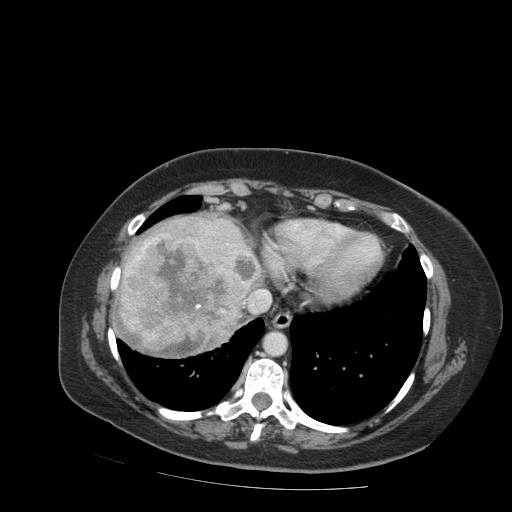
Contrast-enhanced abdominal CT (liver protocol), one axial slice. Slice 79 of 99 in the series (ordered by position). 140 kVp. Soft-tissue window (W 400 / L 40 HU). 2.5 mm slice thickness. 512 × 512 image matrix. Case-level facts recorded for this patient, not image findings: diagnosis: hepatocellular carcinoma (patient treated with transarterial chemoembolisation; whether this scan precedes or follows treatment is not stated here); TNM stage (as recorded): Stage-IVB; Child-Pugh class: A; tumour differentiation: moderately differentiated; tumour nodularity: uninodular.
Outlined on this slice (semi-automatically segmented with operator editing):
- liver parenchyma outside the tumour (the mass and vessels are separate outlines, so this box may not span the whole liver): box from (x=118, y=216) to (x=262, y=342) px
- mass: (x=115, y=236)–(x=256, y=360)
- liver vessels: (x=207, y=231)–(x=250, y=256)